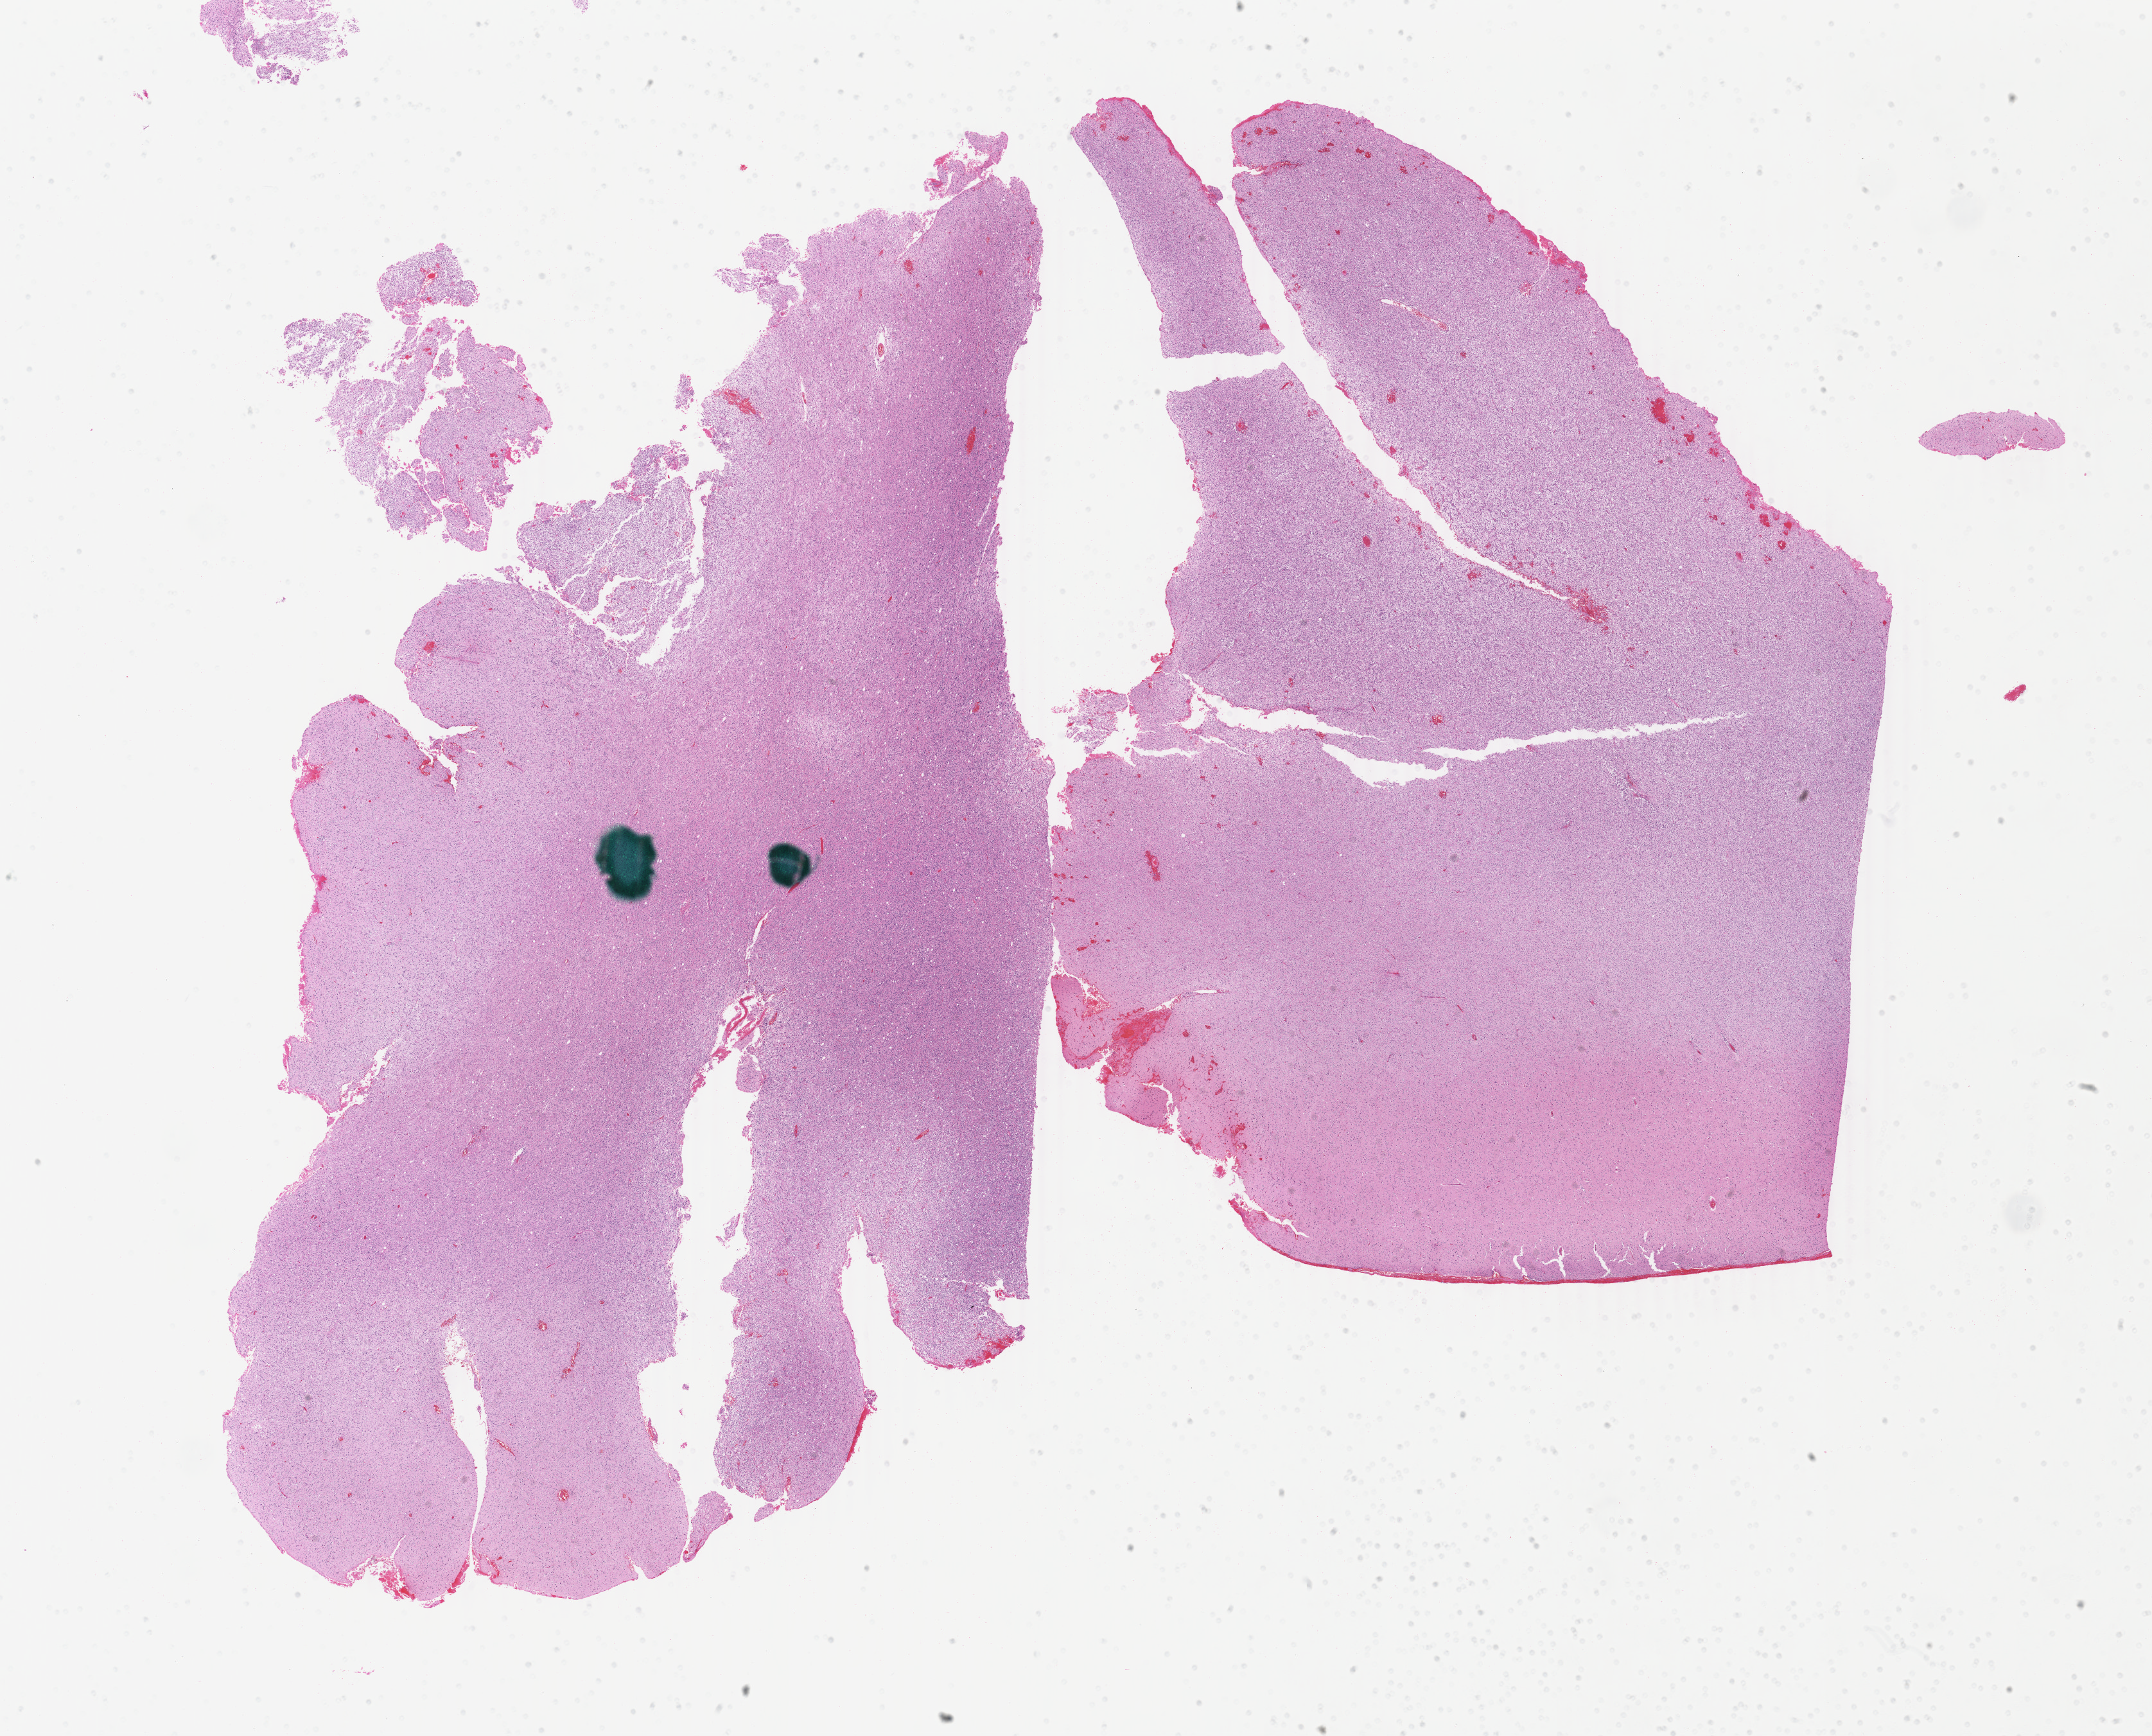
Whole-slide histology image, Hematoxylin and eosin (H&E) stained, shown as a low-resolution overview of the whole scanned area (about 26.7 x 21.5 mm, acquisition: 40x scan), formalin-fixed paraffin-embedded (FFPE) diagnostic section, primary tumour sample from the brain. Female, age 38 years at initial diagnosis. Histologic grade: G3 (poorly differentiated).
Histologic diagnosis: Mixed glioma (cerebrum).